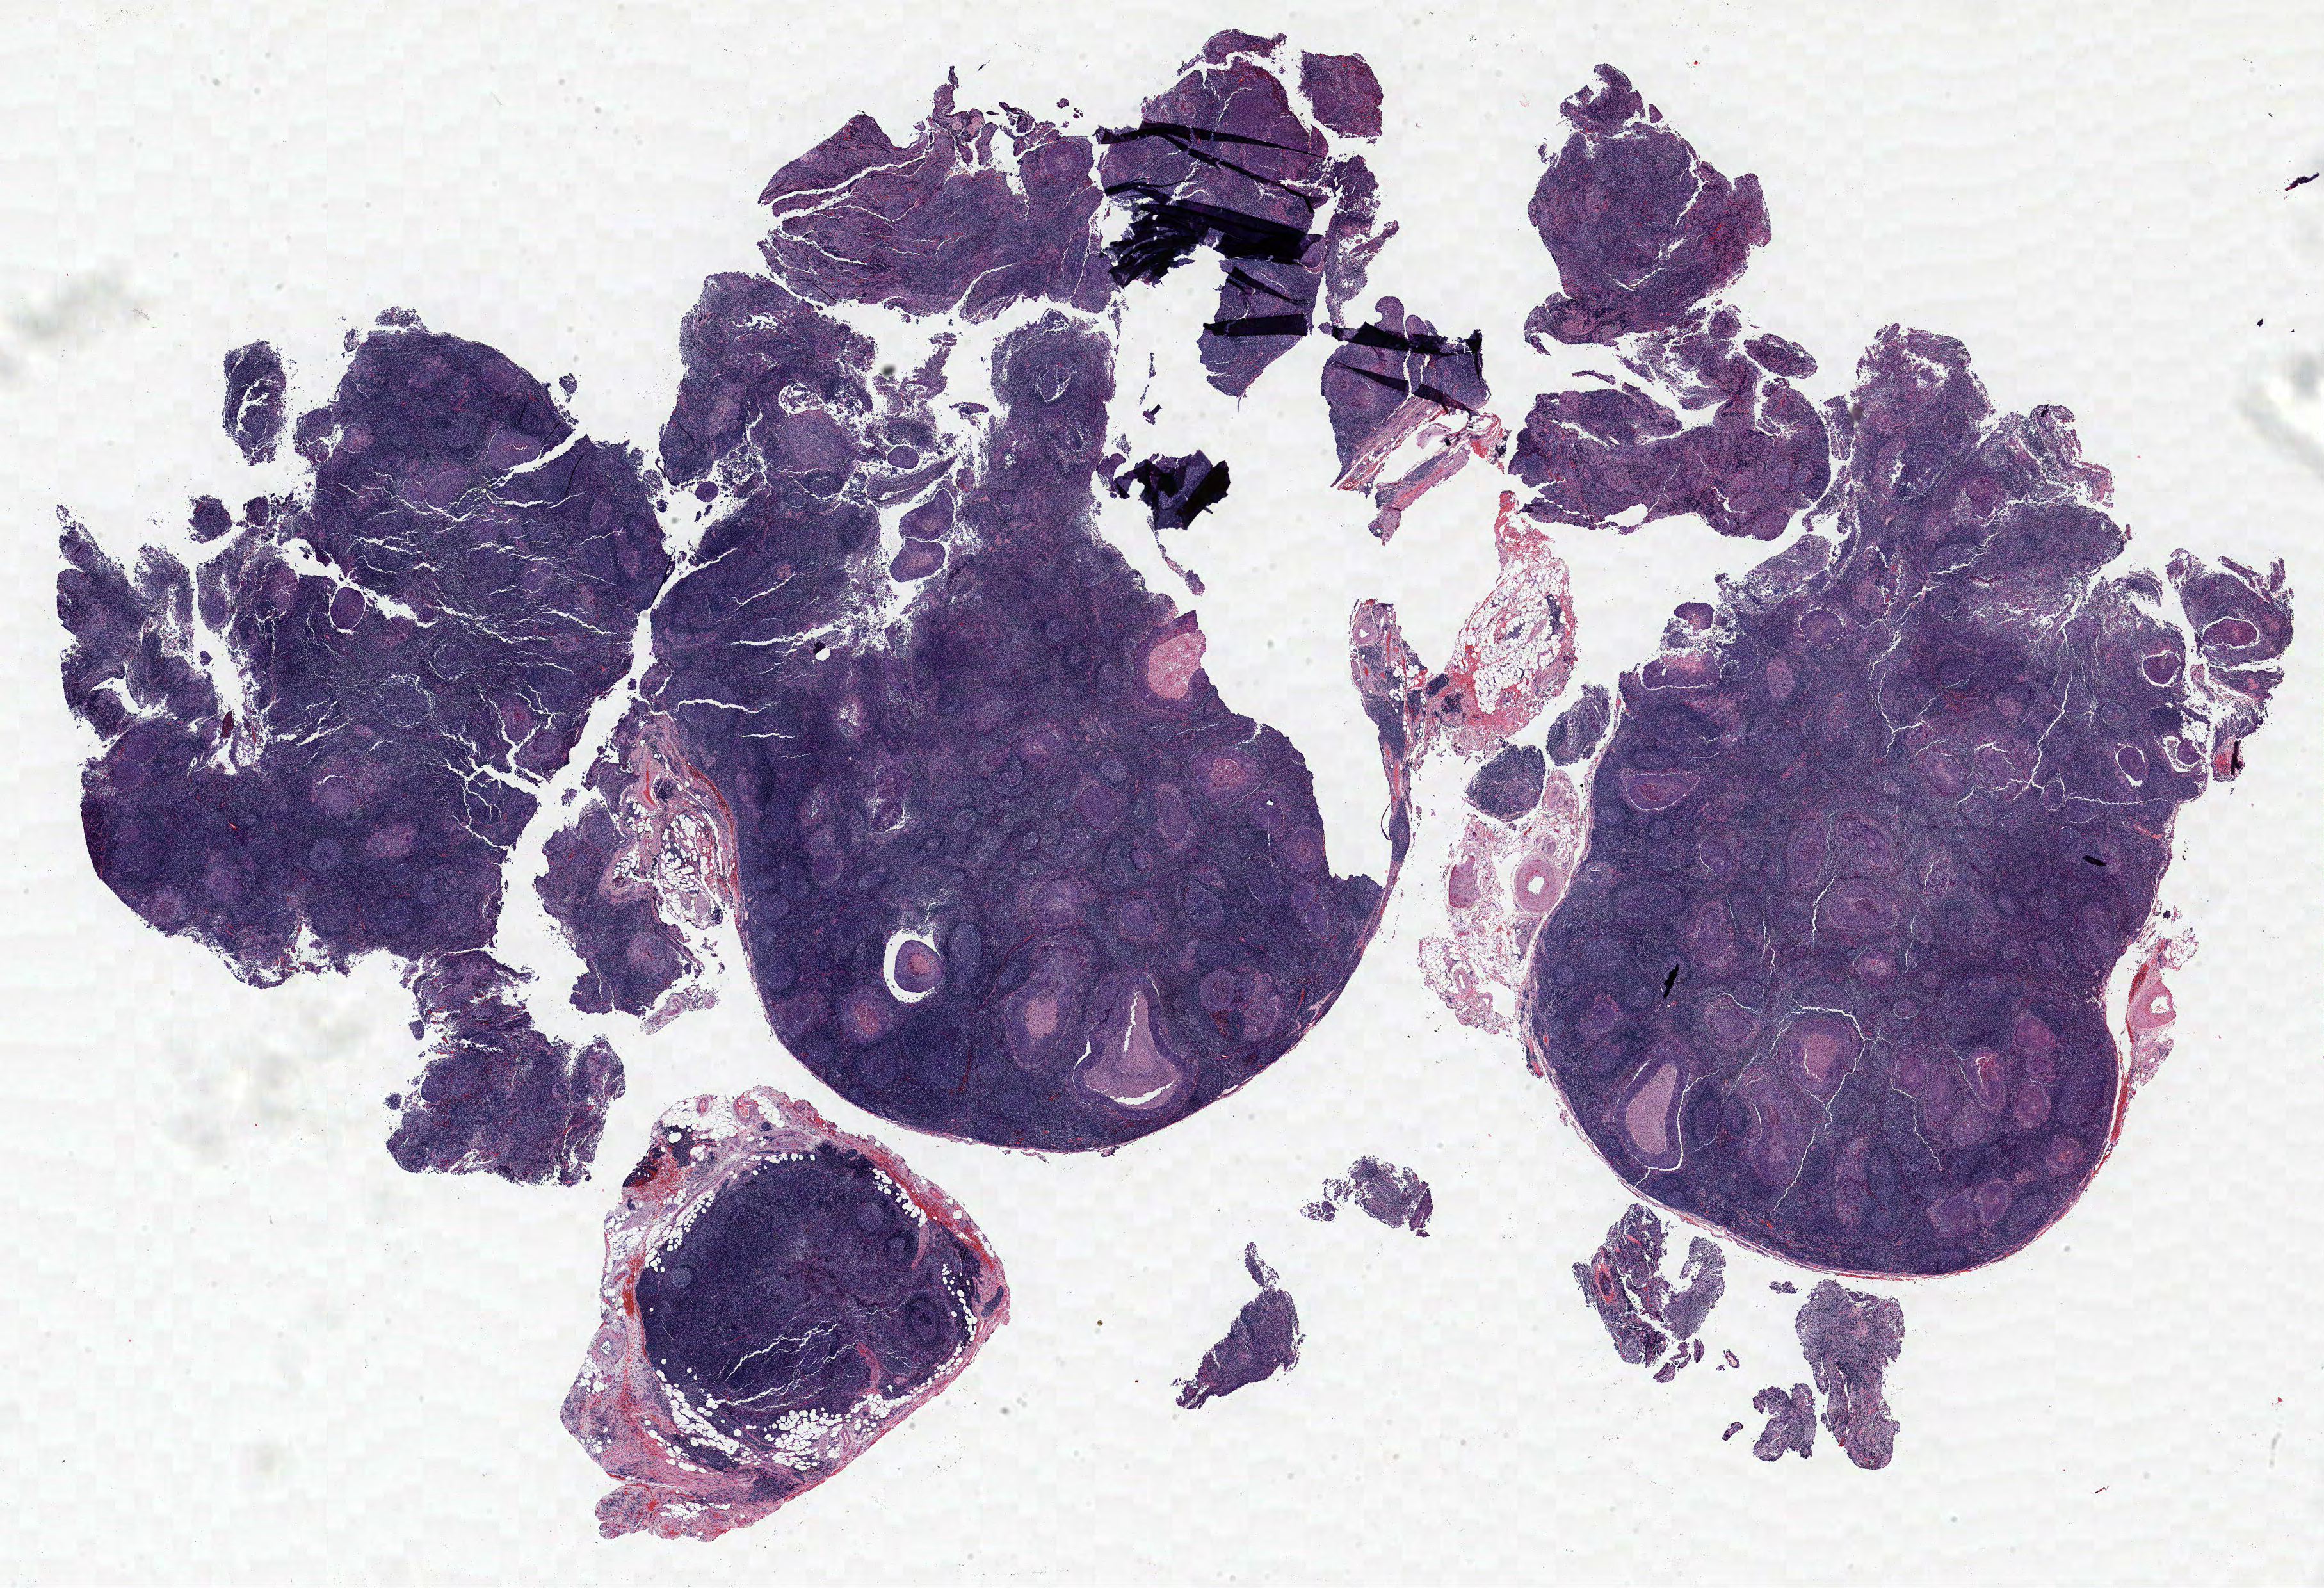
Whole-slide histology image, H&E-stained, a low-resolution overview of the entire scanned area, about 29.0 x 19.8 mm (from a 40x scan). FFPE section. Lung tissue. Female patient, aged 64 at enrolment. Grade: cannot be assessed (GX).
• stage (AJCC 6th edition): IIIA
• participant's lung-cancer diagnosis: Squamous cell carcinoma, NOS (ICD-O-3 8070/3)